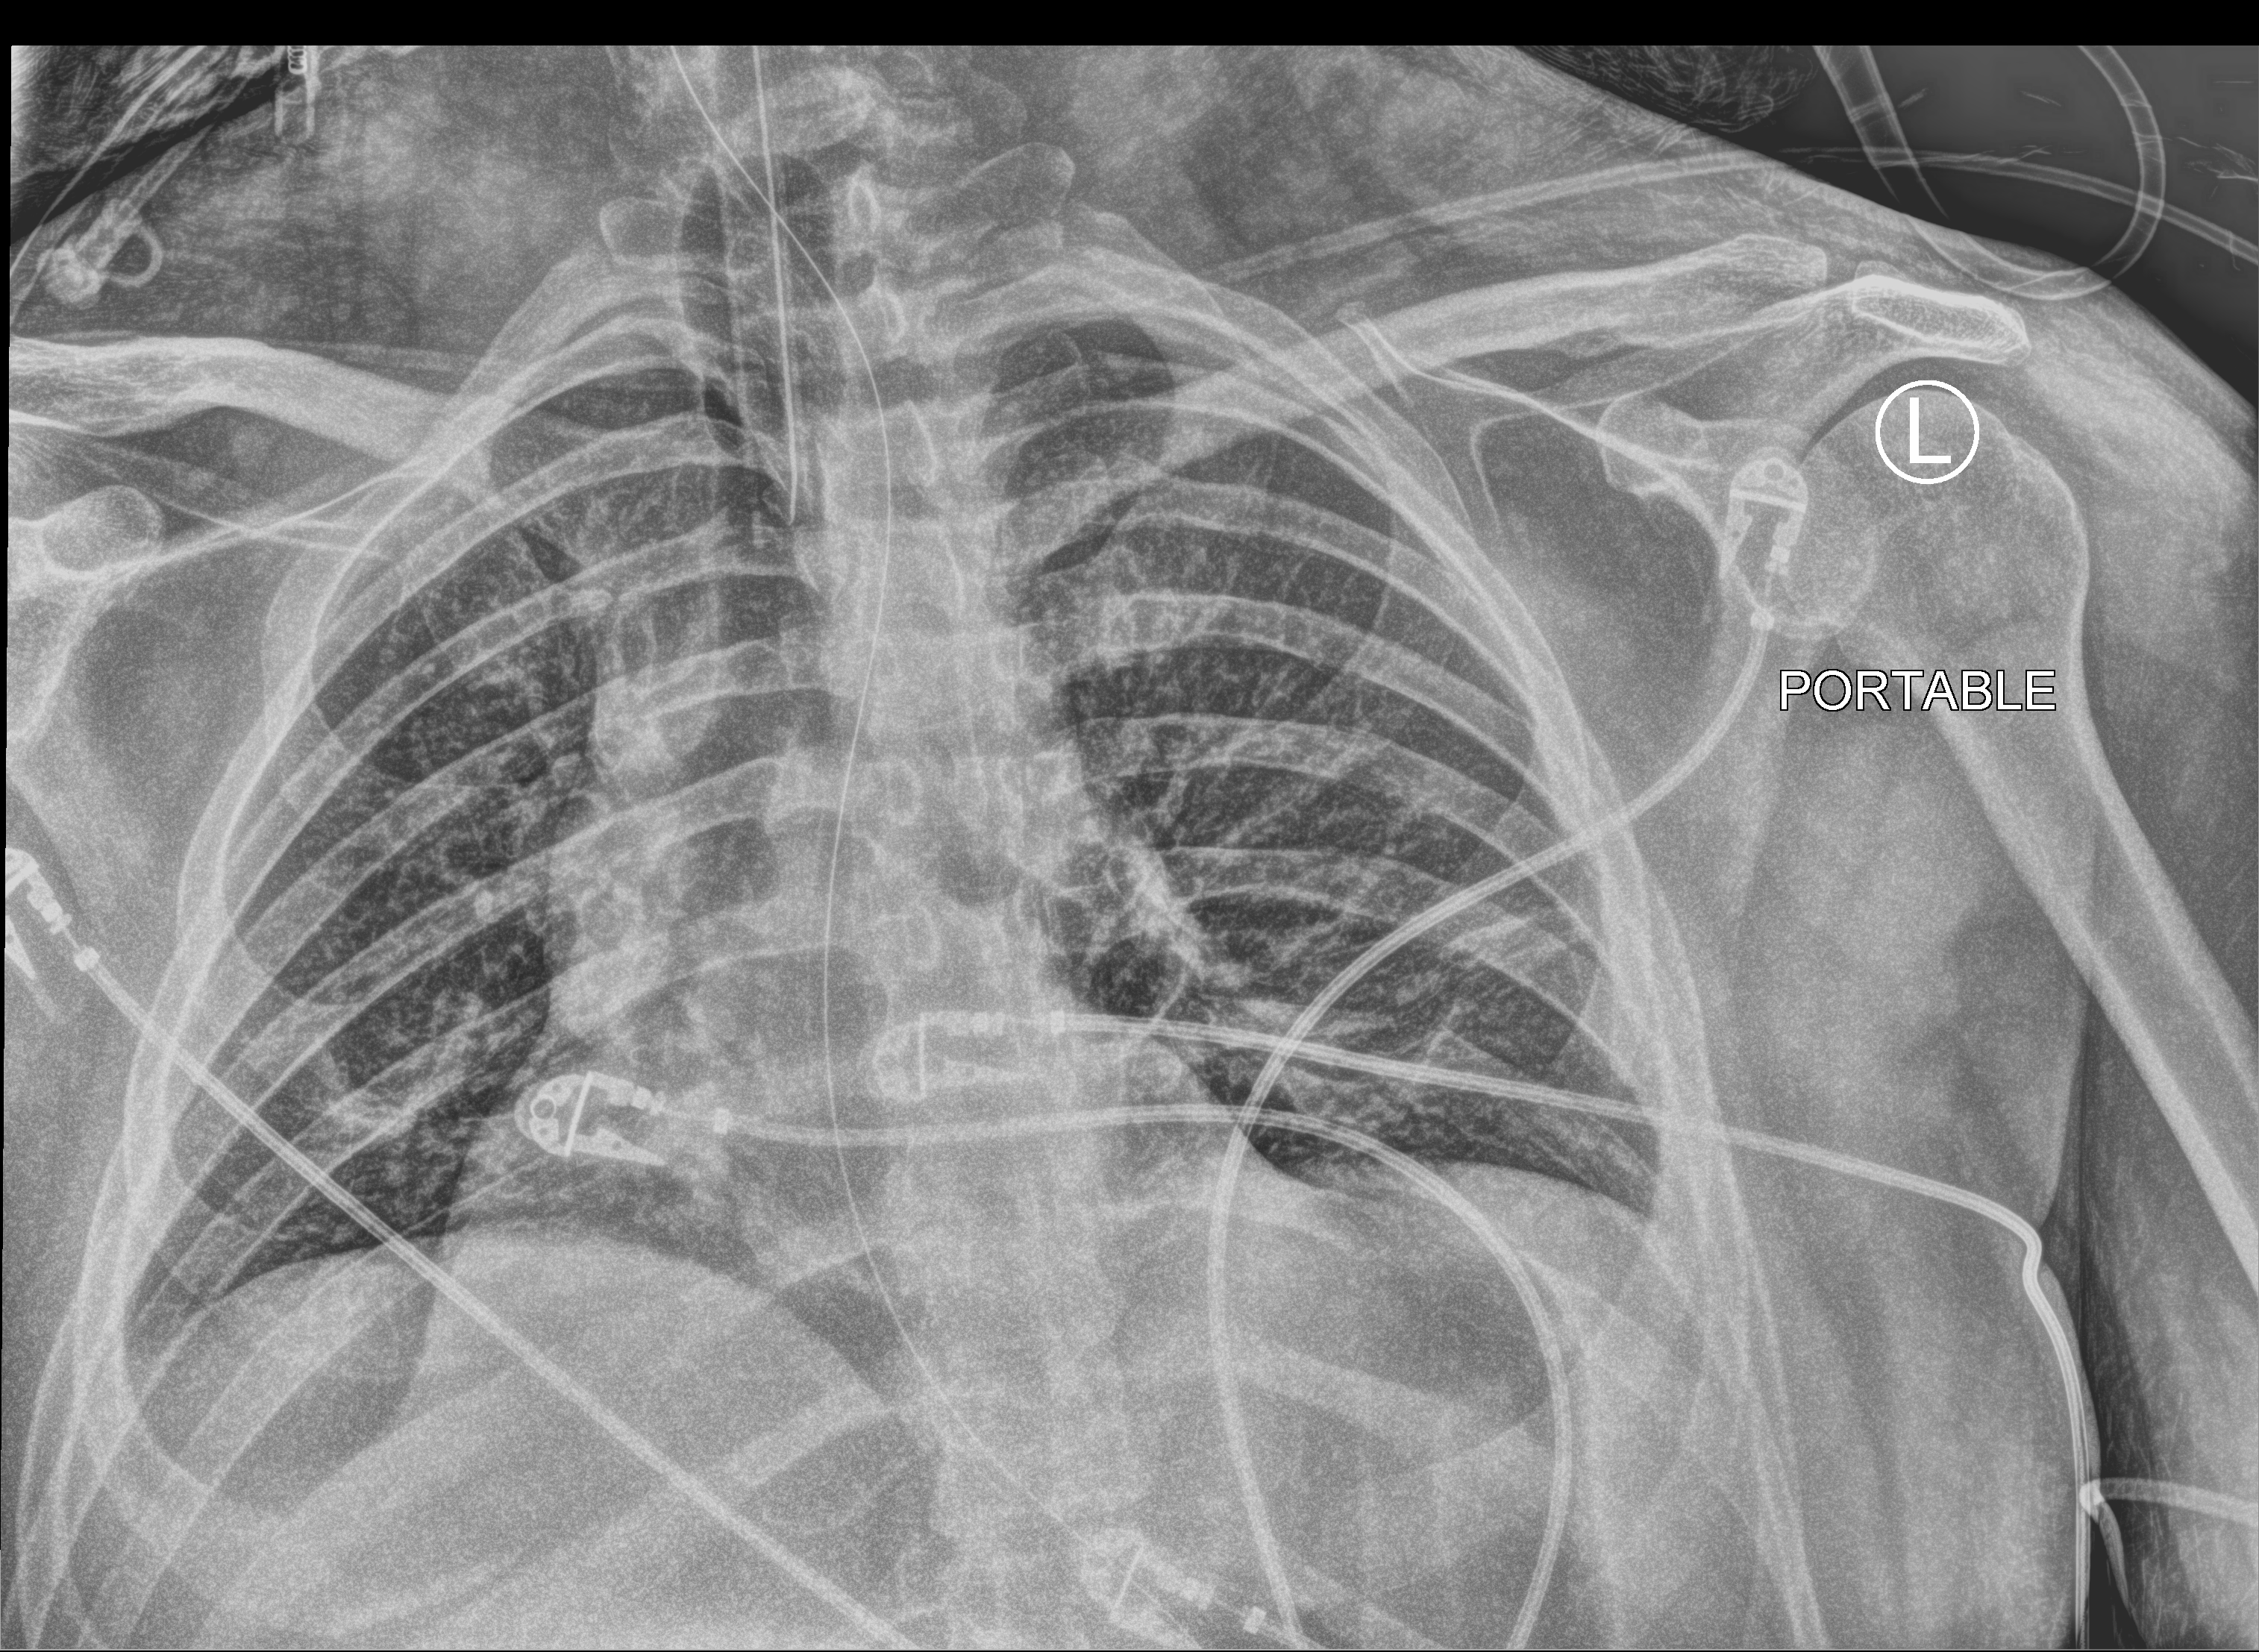
Bedside chest radiograph (computed radiography); anteroposterior (AP) projection. Patient hospitalised with COVID-19; male, aged 18–59 years.
From the hospital-stay record, not from the radiograph (when in the stay this image was taken is not recorded):
- diabetes (admission record): no
- mechanically ventilated during this hospital stay: yes
- admitted to intensive care during this hospital stay: yes